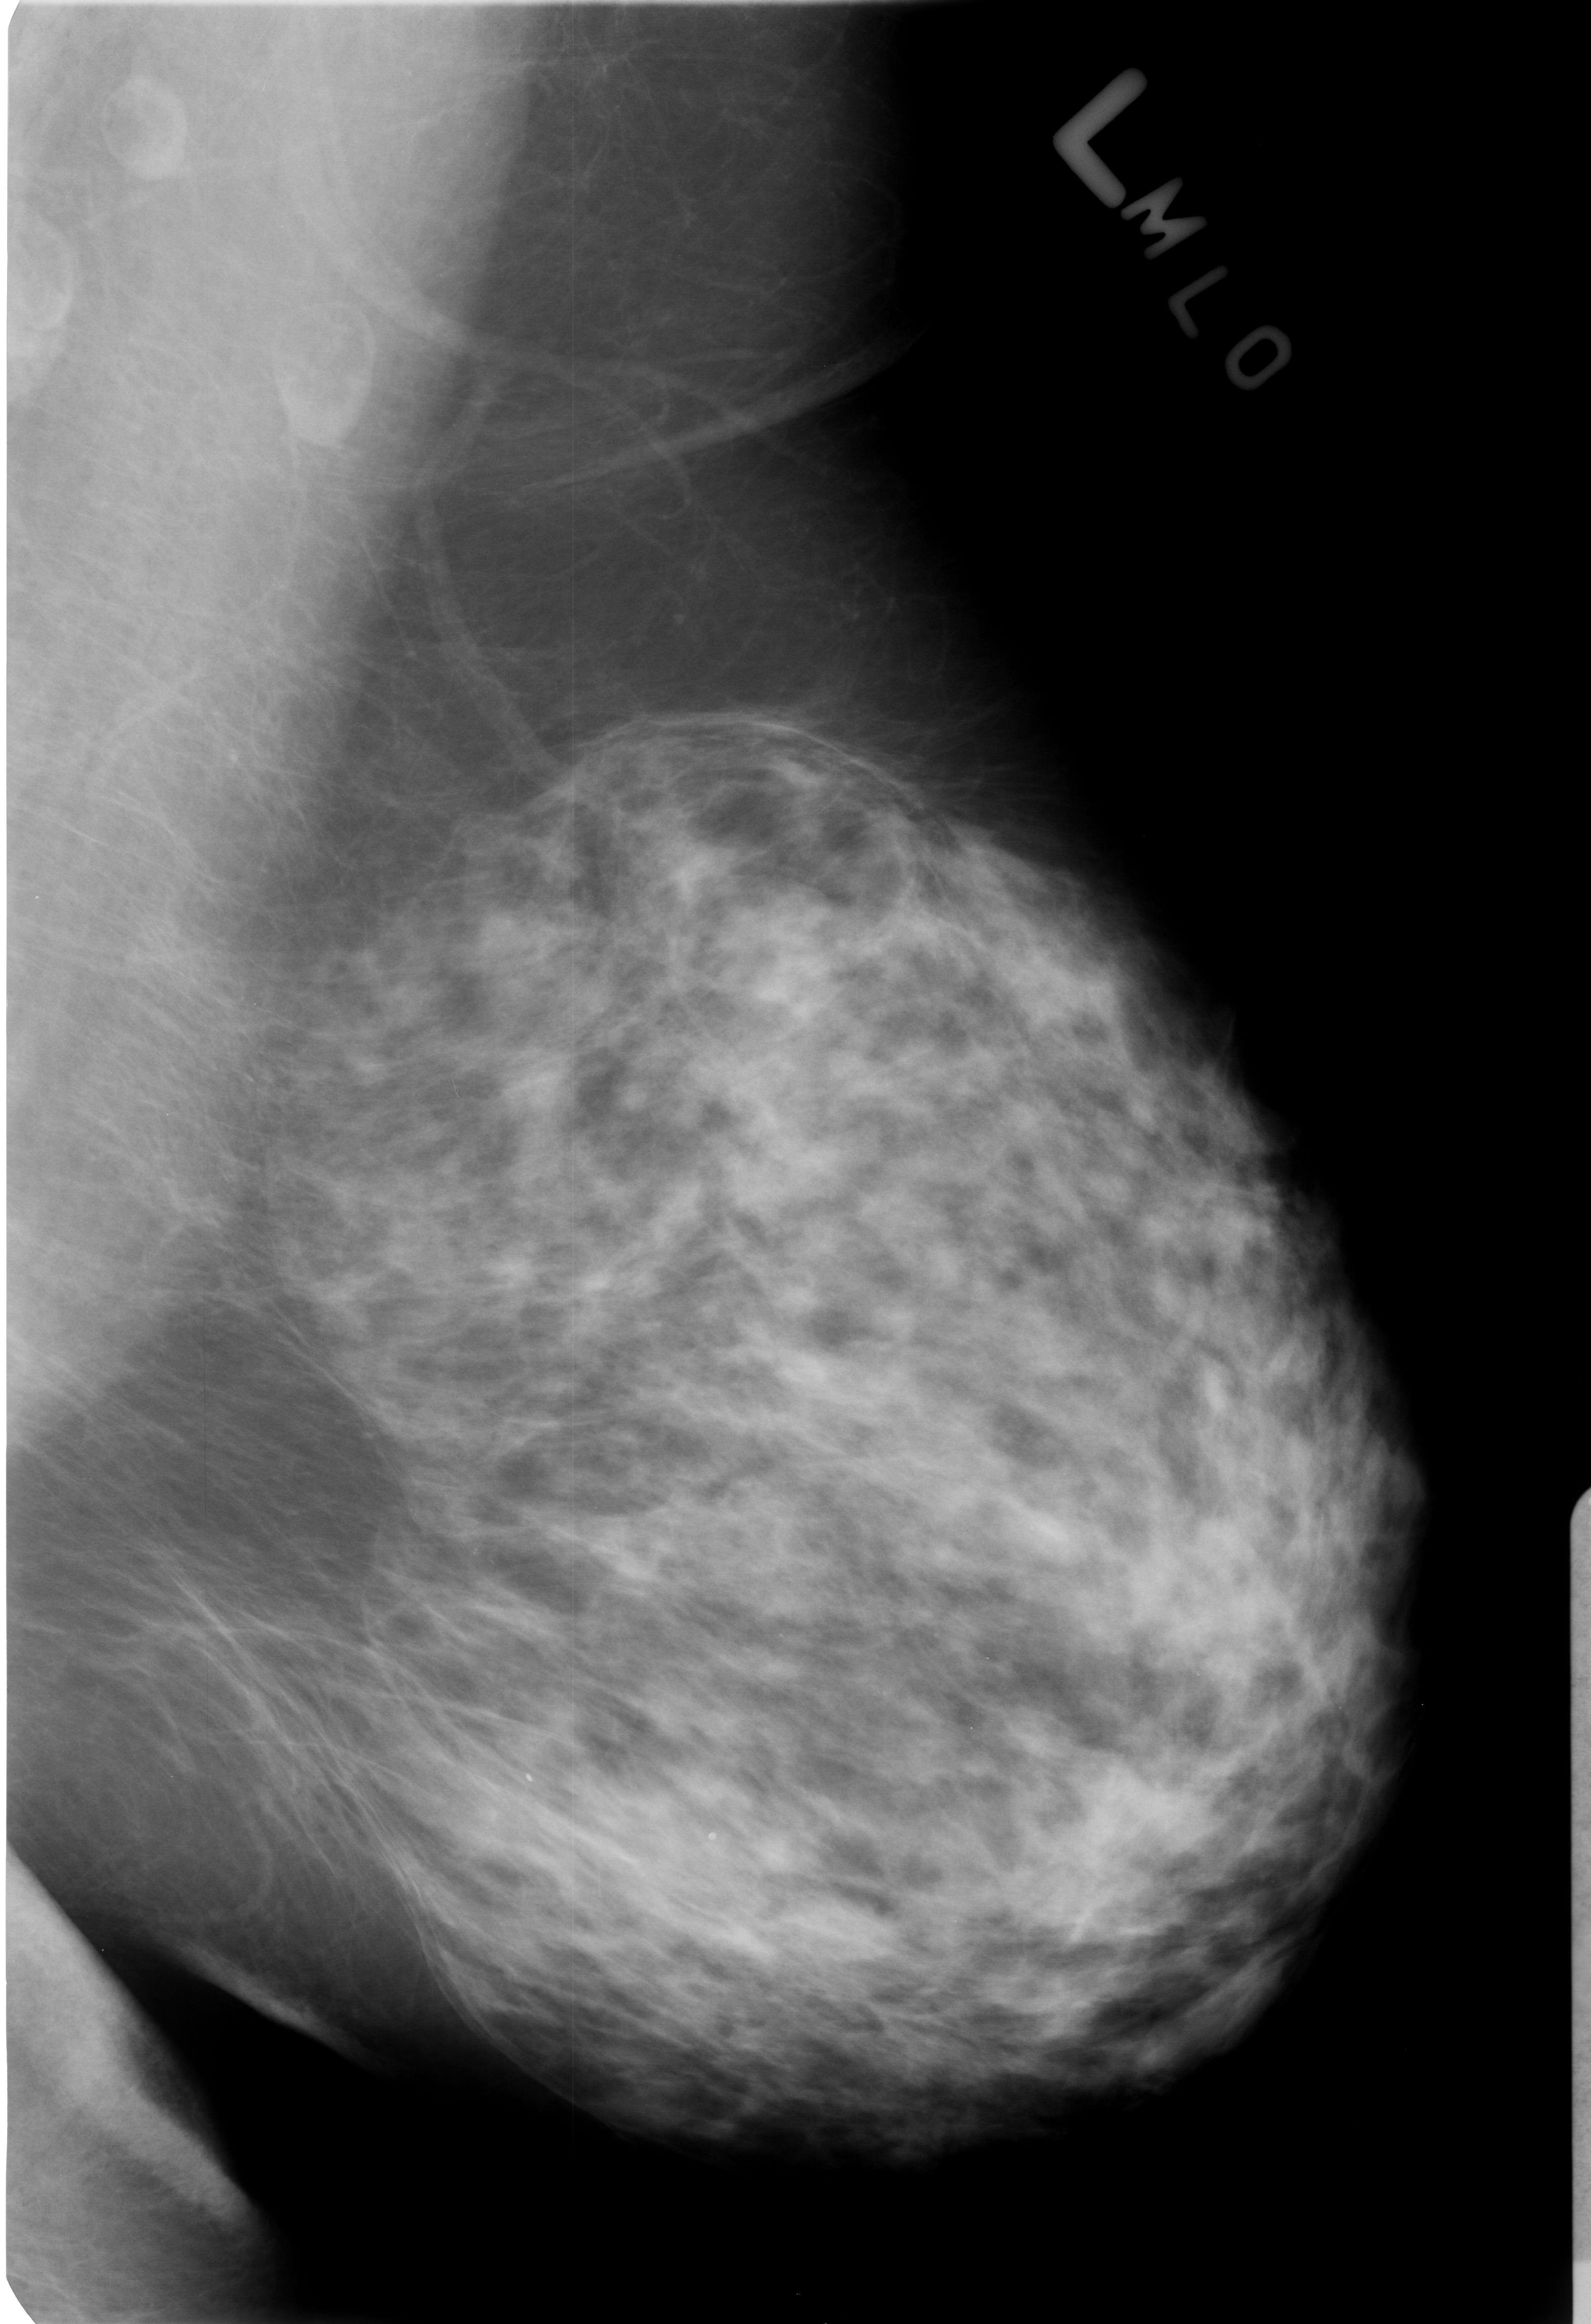
Scanned film-screen mammogram. Left breast. MLO view. BI-RADS breast density category 3 (scale 1–4). 1591 × 2324 image matrix.
Expert-marked regions of interest on this film, with their recorded descriptors:
- Finding 1 of 2: calcifications, morphology lucent center; BI-RADS assessment category 2; outcome (as recorded, no biopsy): benign without callback (not worked up further): bounding box <510,1753,548,1803> (left, top, right, bottom; pixels)
- Finding 2 of 2: calcifications, morphology lucent center; BI-RADS assessment category 2; benign; no additional work-up was recommended (outcome (as recorded, no biopsy): benign without callback): <680,1817,742,1867>